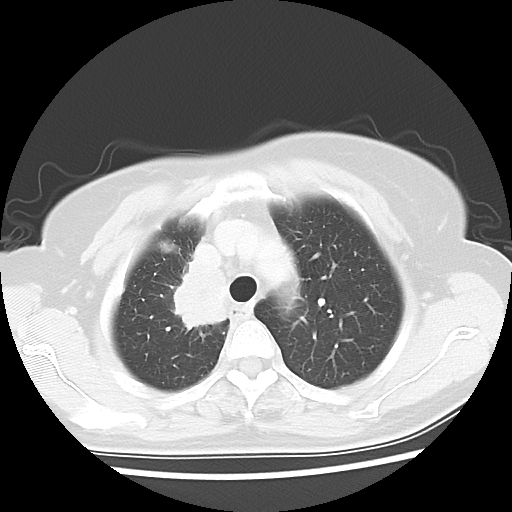
Chest CT, one axial slice. Slice 45 of 56 in the series (ordered by position). Lung window (W 1500 / L -600 HU). 5 mm slice thickness. 512 × 512 image matrix, field of view 314 × 314 mm. Patient: female, 62 years. Case-level facts recorded for this patient, not image findings: clinical TNM (as recorded): T2 N1 M1a.
Structures marked on this image (bounding box drawn by a radiologist):
- lung tumour (recorded histology: adenocarcinoma): bounding box <171,248,234,339> (left, top, right, bottom; pixels)